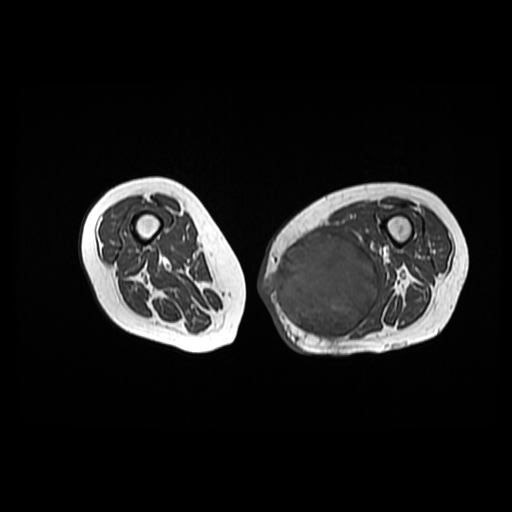
MRI of an extremity soft-tissue mass, one axial slice; position 29 of 42 along the scan axis; 512 × 512 image matrix. Female patient. From the clinical record (not read from this slice): histological type: pleomorphic leiomyosarcoma; grade: high; site of the primary tumour: left thigh.
Structures marked on this image (expert manual segmentation):
- gross tumour volume including surrounding oedema: box from (x=264, y=231) to (x=382, y=340) px
- gross tumour volume (mass): (x=264, y=231)–(x=380, y=340)